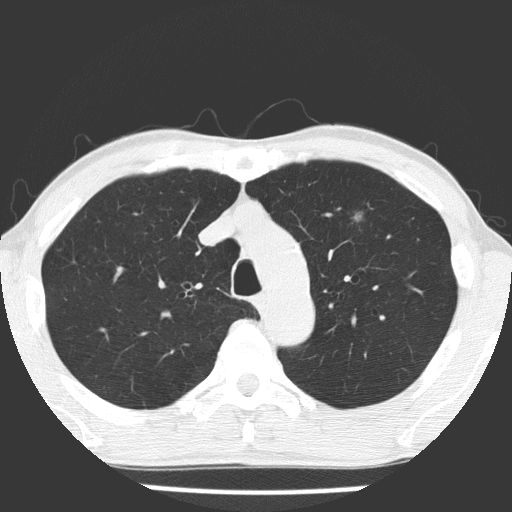
Chest CT (low-dose screening protocol), one axial image, baseline annual screen, lung window (W 1500 / L -600 HU), 120 kVp, slice 50 of 177 in the series. Male participant, aged 66 years at enrolment.
Expert reader's lesion annotation, box from (x=331, y=198) to (x=380, y=243) px. Screening reader's record for this exam (one nodule recorded; not confirmed to be the boxed lesion): non-calcified nodule or mass ≥4 mm, left upper lobe, 8 × 8 mm, poorly defined margins, mixed attenuation.